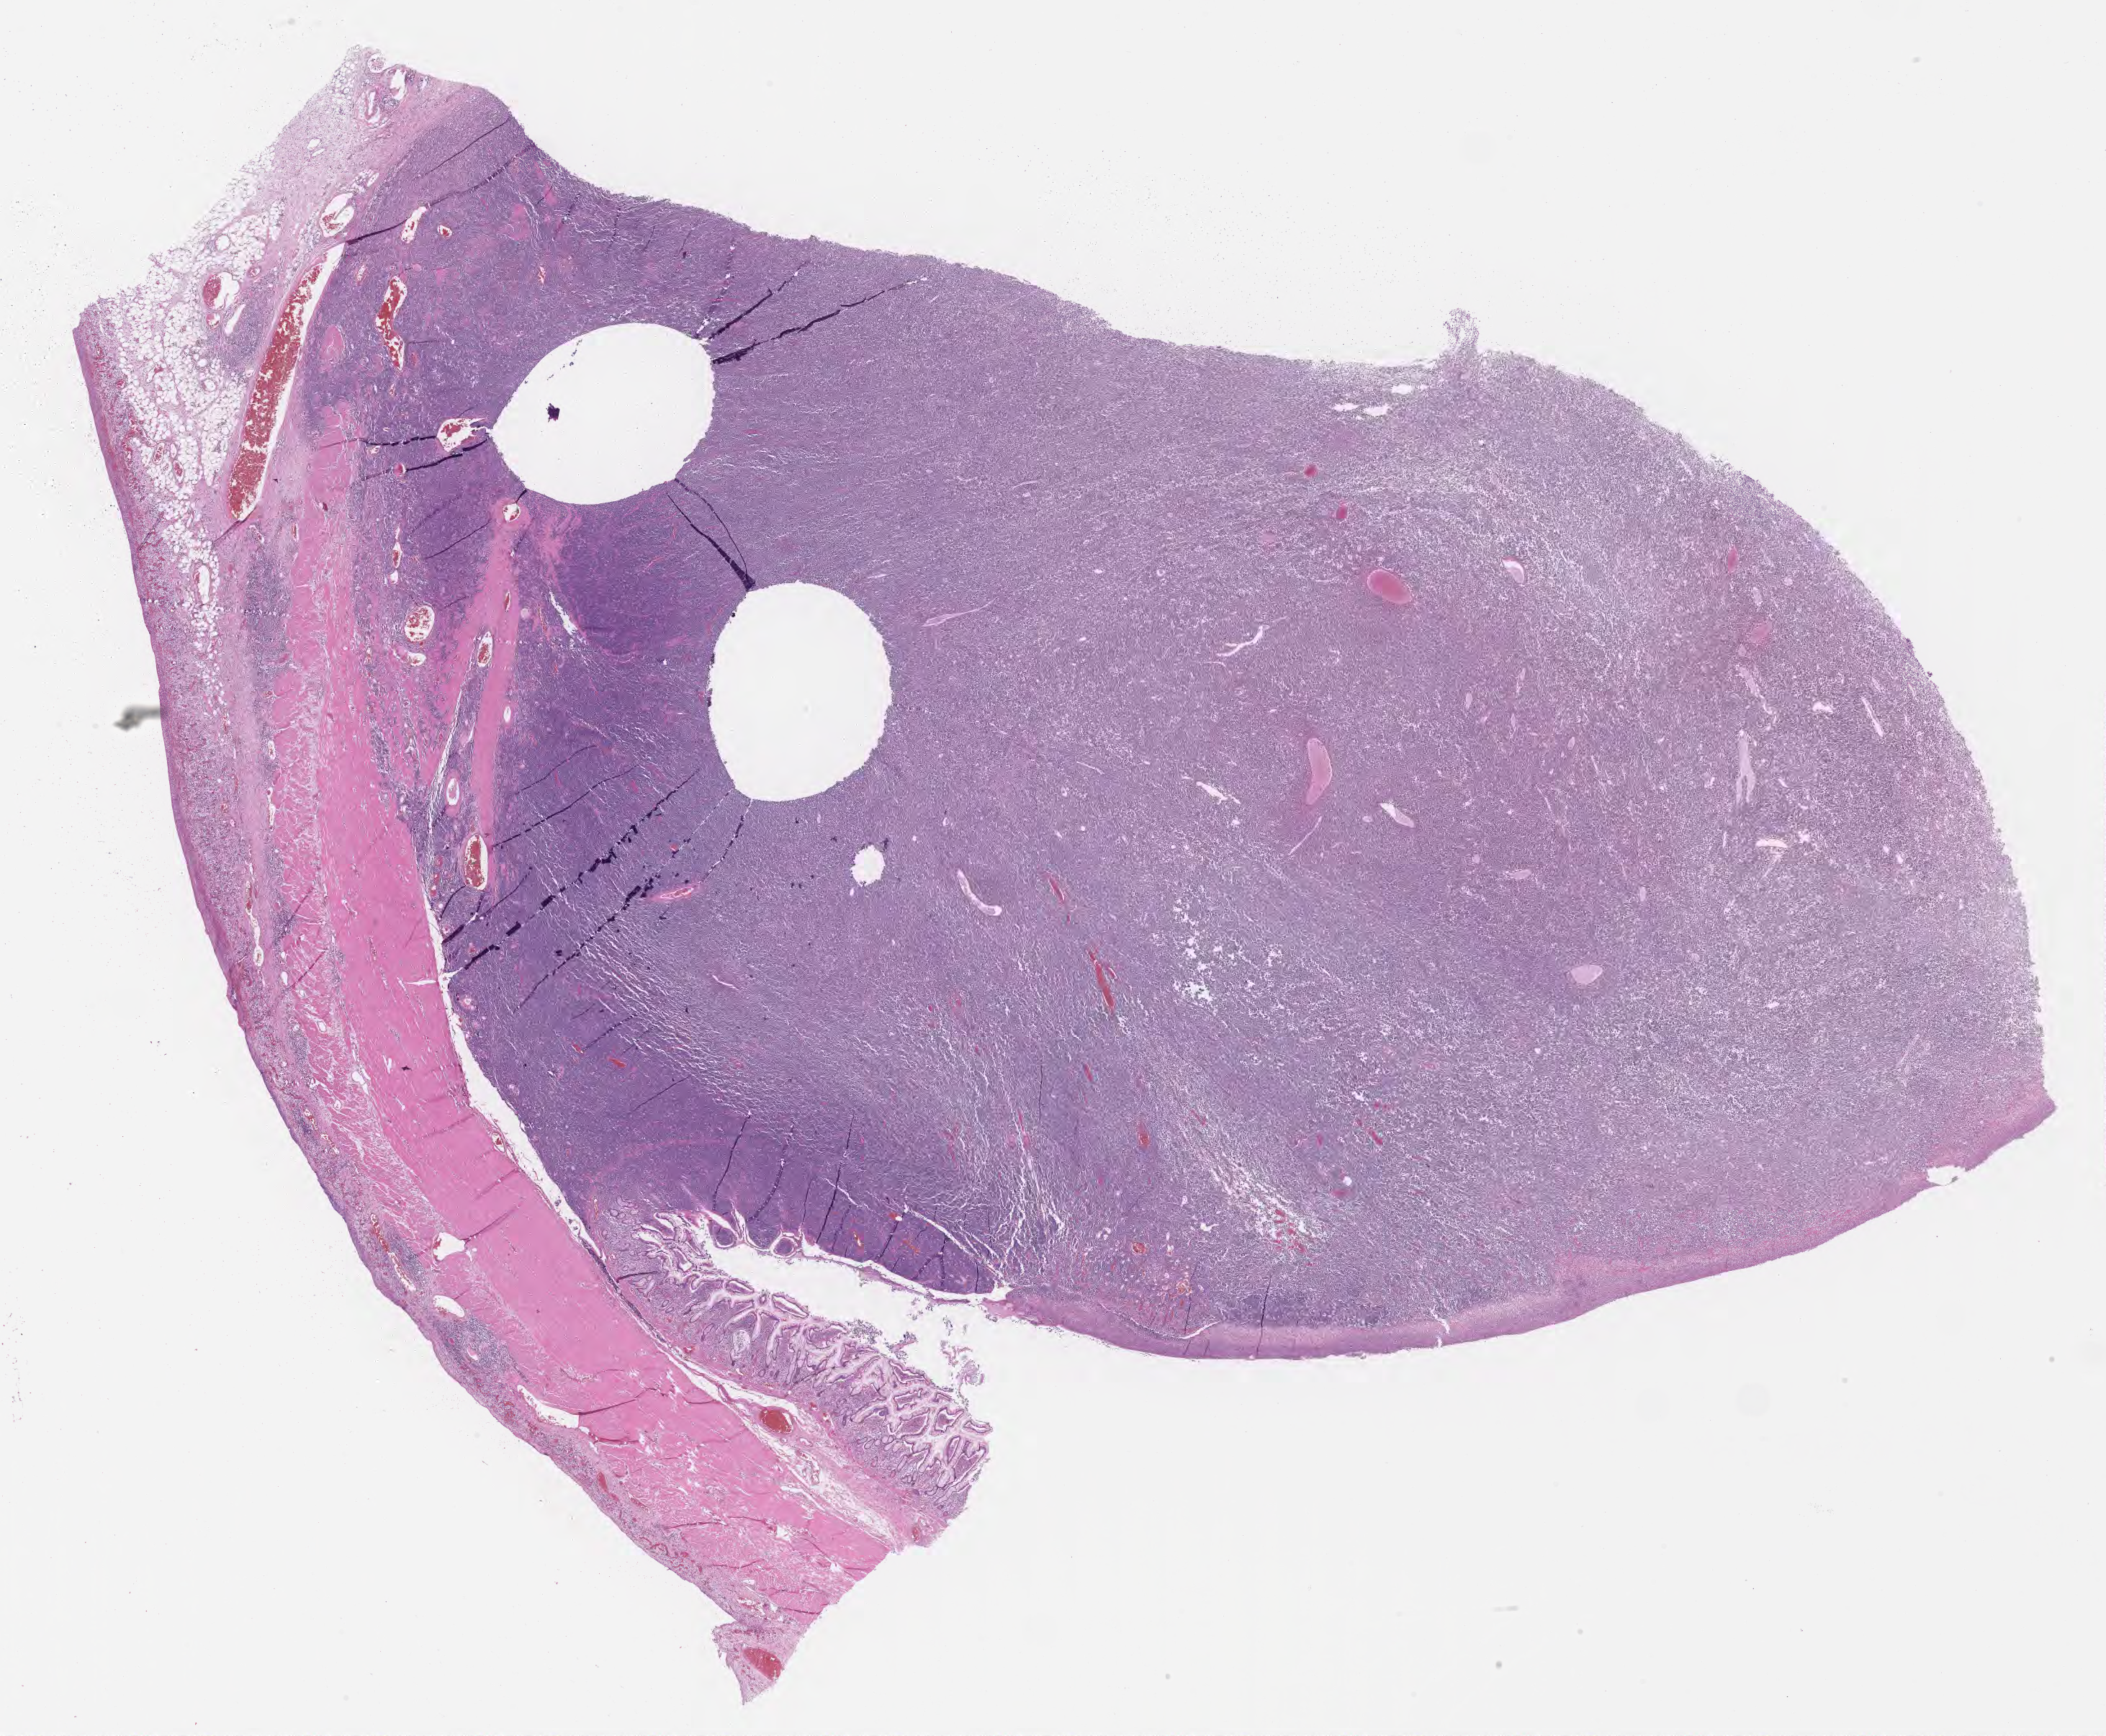
Whole-slide image, hematoxylin and eosin (H&E) stain, whole scanned area (about 23.6 x 19.5 mm) shown as a low-resolution overview, specimen: tumor tissue. Patient female; aged 15.
Histologic diagnosis: Burkitt lymphoma, NOS.